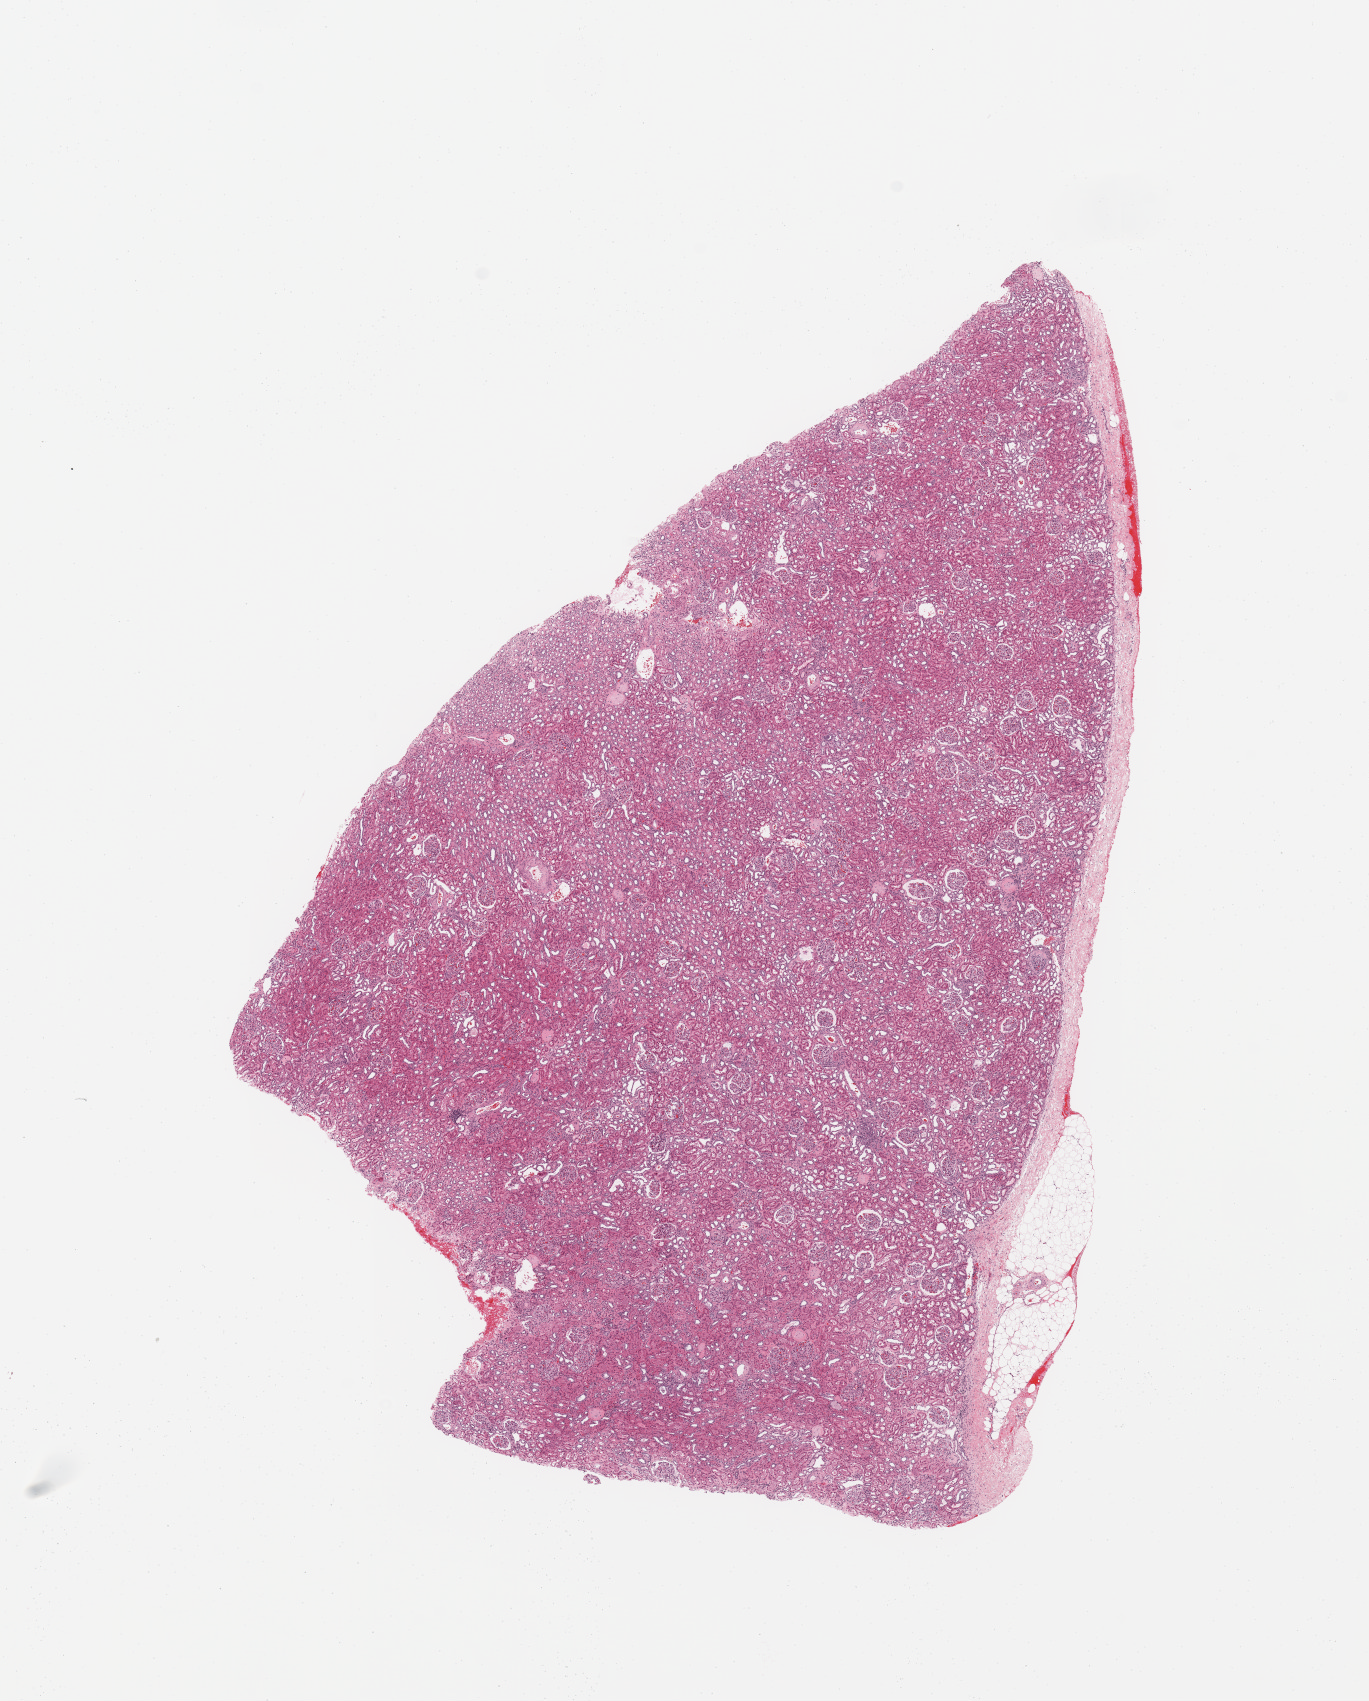
Whole-slide histology image, H&E — low-resolution overview of the scanned area, about 10.8 x 13.5 mm (acquisition: 20x scan). Normal (non-tumour) tissue sample, sampled site: kidney. 60-year-old female patient.
- this section: normal (non-tumour) tissue from the same patient
- patient diagnosis: Renal cell carcinoma, NOS